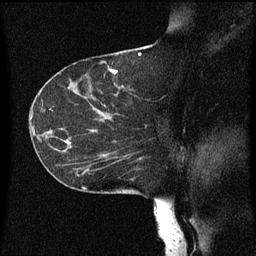
Breast MRI (dynamic contrast-enhanced), one sagittal slice. Position 33 of 60 along the scan axis. Dynamic contrast-enhanced series, image 2 of 3 at this slice position (ordered by acquisition). 1.5 T. TE 4.2 ms, TR 8 ms. 256 × 256 image matrix. Female patient, age 55 years.
Structures marked on this image (semi-automatic segmentation, software-assisted and operator-edited):
- analysis volume of interest (the breast-tissue region the enhancement analysis was run in; not a lesion): box from (x=46, y=124) to (x=149, y=183) px
- tumour enhancement mask (voxels above the 70 % enhancement threshold inside the analysis volume of interest): (x=78, y=130)–(x=107, y=177)